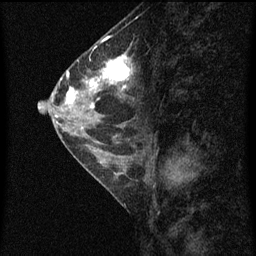
Breast MRI (dynamic contrast-enhanced), one sagittal slice. Slice 29 of 60 in the series (ordered by position). Dynamic contrast-enhanced series, image 2 of 4 at this slice position (ordered by acquisition). 1.5 T. TE 4.2 ms, TR 8 ms. 2 mm slice thickness. 256 × 256 image matrix, field of view 180 × 180 mm. Patient: female, 56 years.
Structures marked on this image (semi-automatically segmented with operator editing):
- analysis volume of interest (the breast-tissue region the enhancement analysis was run in; not a lesion): bounding box (x1, y1, x2, y2) in pixels: (56, 52, 135, 115)
- tumour enhancement mask (voxels above the 70 % enhancement threshold inside the analysis volume of interest): (67, 54, 133, 109)